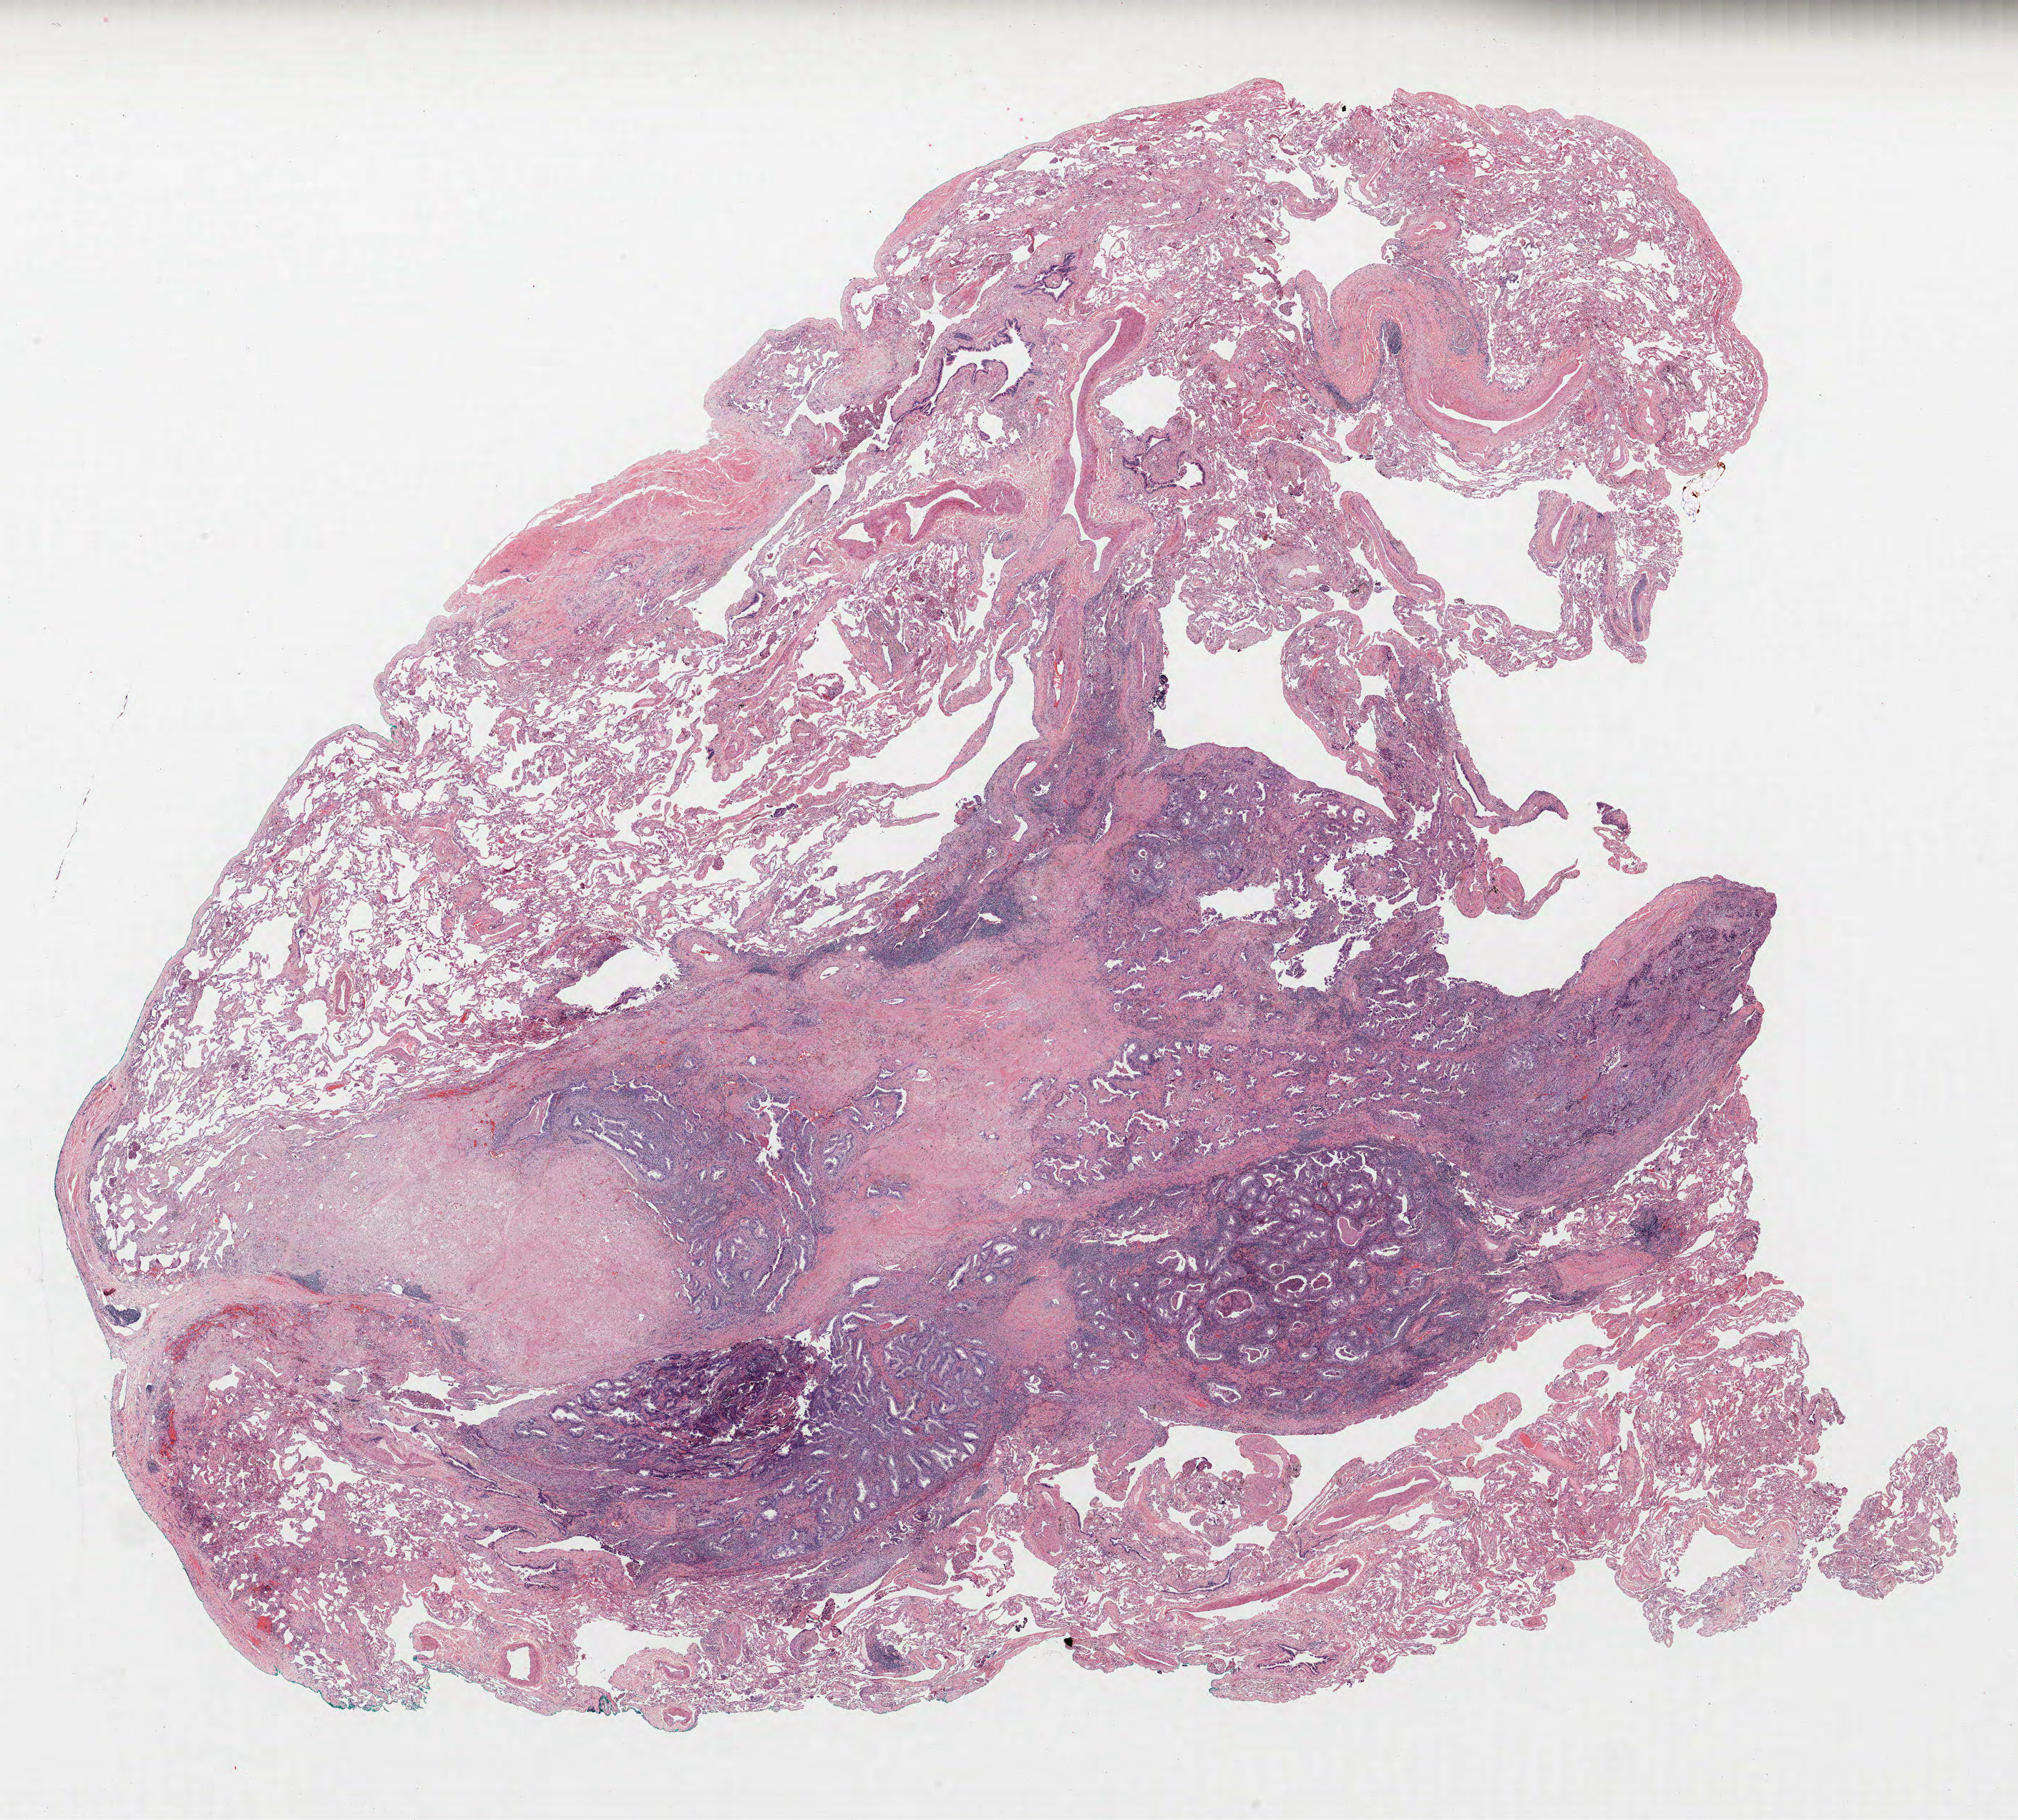
Whole-slide histology image, Hematoxylin and eosin (H&E) stained, shown as a low-resolution overview of the whole scanned area (about 22.6 x 20.3 mm, slide scanned at 40x). FFPE section. Lung tissue. Male patient, aged 63 at enrolment. Current smoker at enrolment. Grade: moderately differentiated (G2).
- participant's lung-cancer diagnosis: Adenocarcinoma, NOS (ICD-O-3 8140/3)
- tumour size (pathology): 17 mm
- primary tumour location (clinical record): right upper lobe
- stage (AJCC 6th edition): IIIB
- ICD-O-3 topography: upper lobe of lung (C34.1)